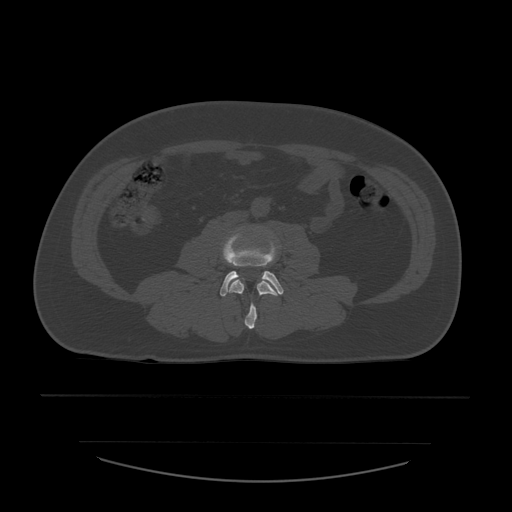
CT including the spine, one axial slice; position 159 of 532 along the scan axis; bone window (W 1800 / L 400 HU); 1.25 mm slice thickness; 512 × 512 image matrix, field of view 441 × 441 mm. Patient age 44 years. Case-level facts recorded for this patient, not image findings: primary cancer: soft tissue sarcoma.
Outlined on this slice (semi-automatic segmentation, software-assisted and operator-edited):
- L3 vertebra: bounding box <228,279,278,329> (left, top, right, bottom; pixels)
- L4 vertebra: <220,236,284,297>